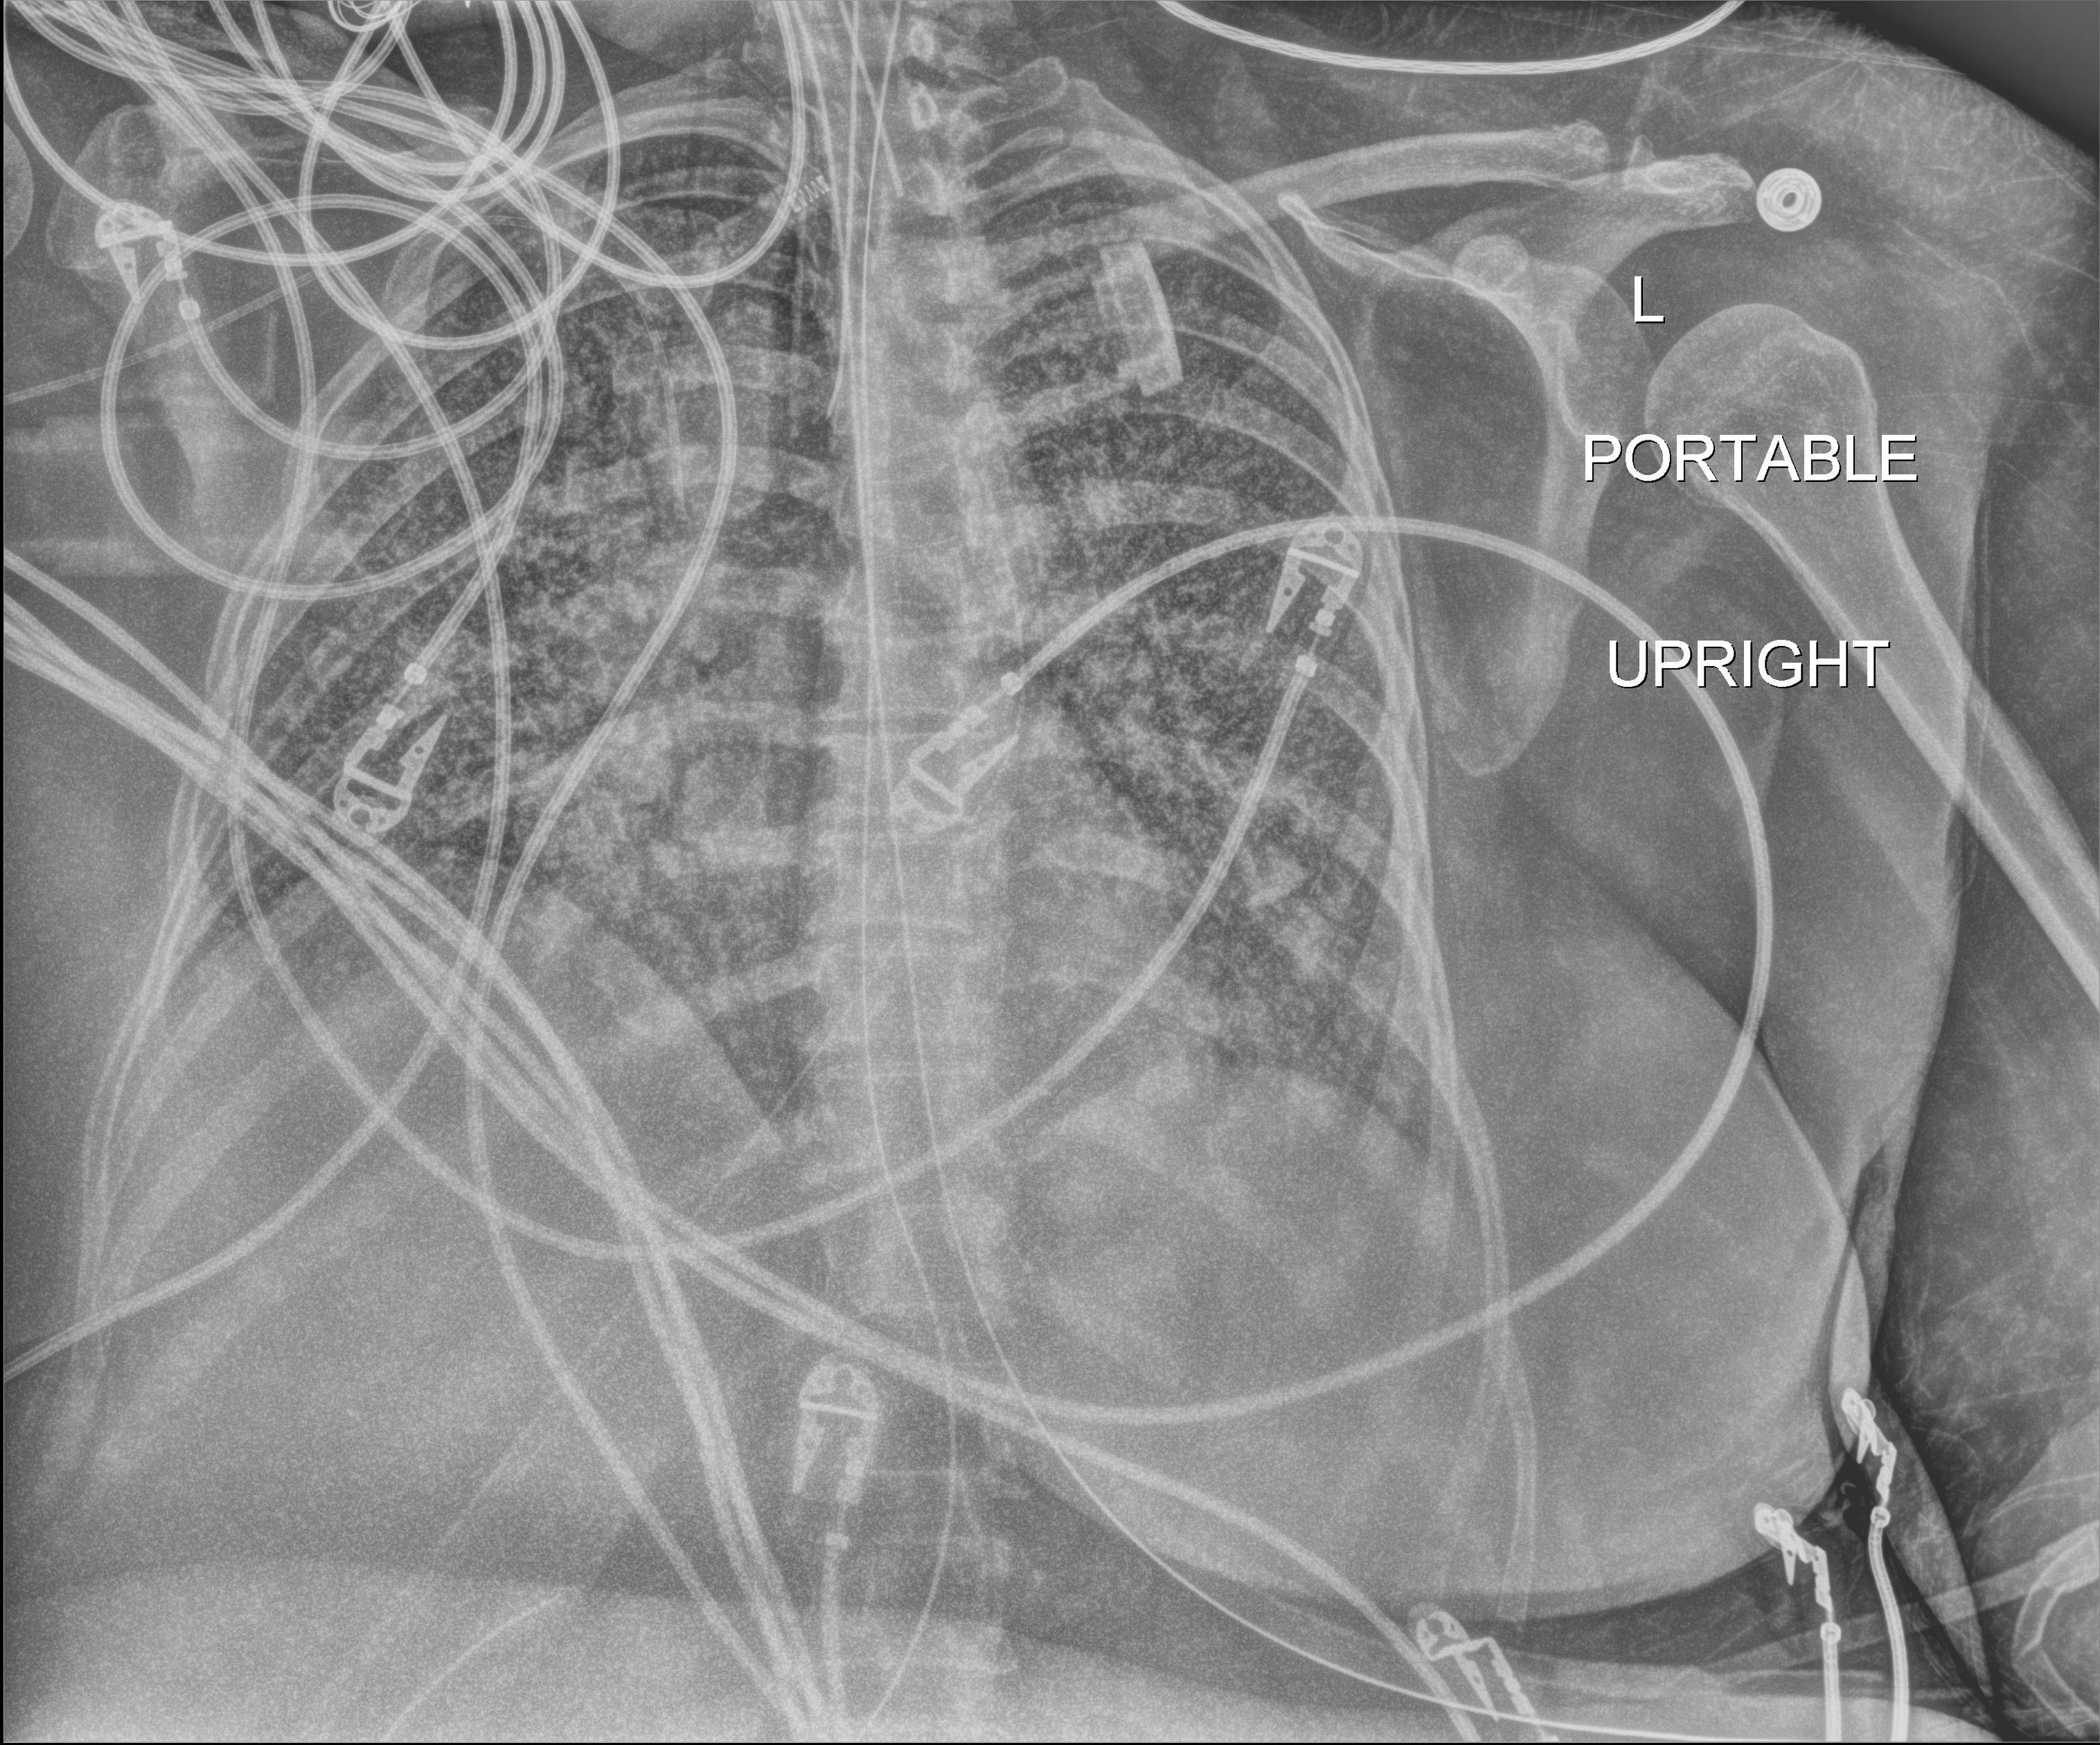
Chest X-ray (portable); anteroposterior (AP) projection. Female patient hospitalised with COVID-19, age 18–59 years.
Hospital-stay facts (about this admission, not read from this image; timing relative to this image not recorded):
- admitted to intensive care during this hospital stay: yes
- length of hospital stay: 95 days